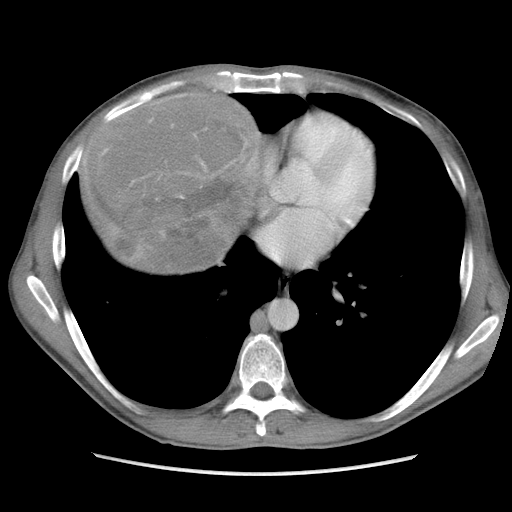
Contrast-enhanced abdominal CT, one axial slice. Position 99 of 115 along the scan axis. Soft-tissue window (W 400 / L 40 HU). 5 mm slice thickness. 512 × 512 image matrix, field of view 360 × 360 mm. Male patient. Case-level facts recorded for this patient, not image findings: diagnosis: adrenocortical carcinoma; tumour side: right adrenal; Ki-67 index: 13 %; stage (as recorded): 3.
Annotated regions visible in this slice (semi-automatically segmented with operator editing):
- mass: bounding box (x1, y1, x2, y2) in pixels: (91, 95, 262, 273)